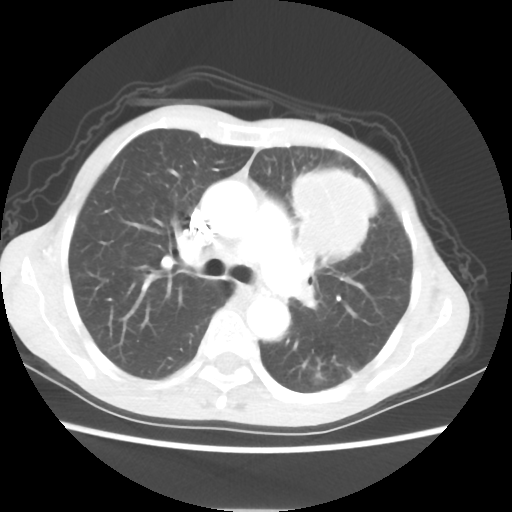
Chest CT, one axial slice. Reconstruction kernel STANDARD. 80 kVp. Lung window (W 1500 / L -600 HU). 5 mm slice thickness. 512 × 512 image matrix, field of view 331 × 331 mm. Female patient, age 60 years. From the clinical record (not read from this slice): clinical TNM (as recorded): T4 N1 M0.
Annotated regions visible in this slice (bounding box drawn by a radiologist):
- lung tumour (recorded histology: adenocarcinoma): box from (x=292, y=166) to (x=376, y=273) px